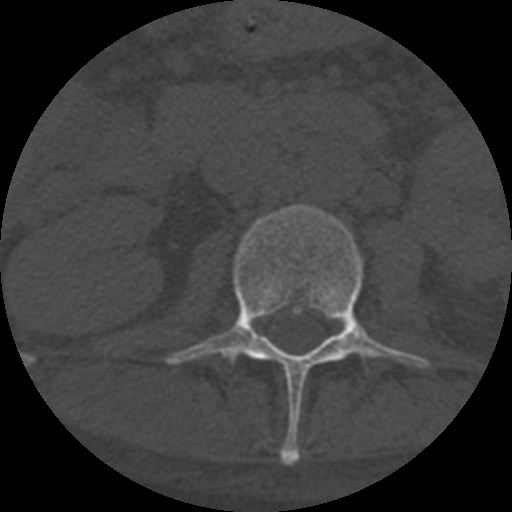
CT including the spine, one axial slice; reconstruction kernel STANDARD; 120 kVp; one of 3 acquisitions stored at this slice position; bone window (W 1800 / L 400 HU); 512 × 512 image matrix. Patient age 55 years. From the clinical record (not read from this slice): primary cancer: colon.
Outlined on this slice (semi-automatic segmentation, software-assisted and operator-edited):
- L2 vertebra: box from (x=166, y=205) to (x=430, y=464) px